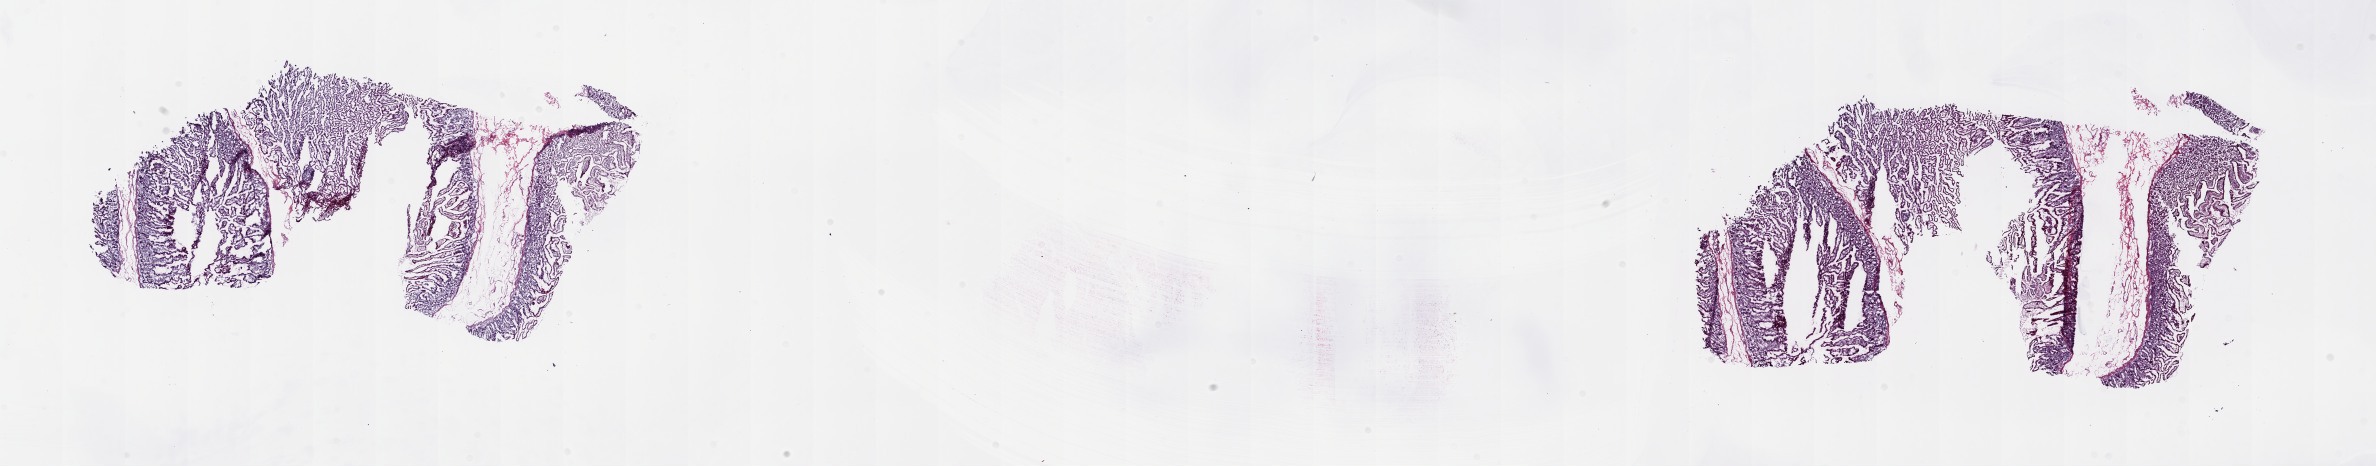
Whole-slide histology image, H&E — low-resolution overview of the scanned area, about 37.7 x 7.4 mm (slide scanned at 20x). Frozen section. Sample: solid tissue normal (non-tumour tissue), bile duct. Male patient. Pathologist review of this section (percent, as recorded): tumour cells 0%, tumour nuclei 0%, normal cells 65%, stromal cells 35%, necrosis 0%. Inflammatory infiltration, as recorded: lymphocyte infiltration 10%, monocyte infiltration 1%, neutrophil infiltration 0%.
This section: solid tissue normal sample (biorepository sample class). Patient diagnosis: Cholangiocarcinoma.